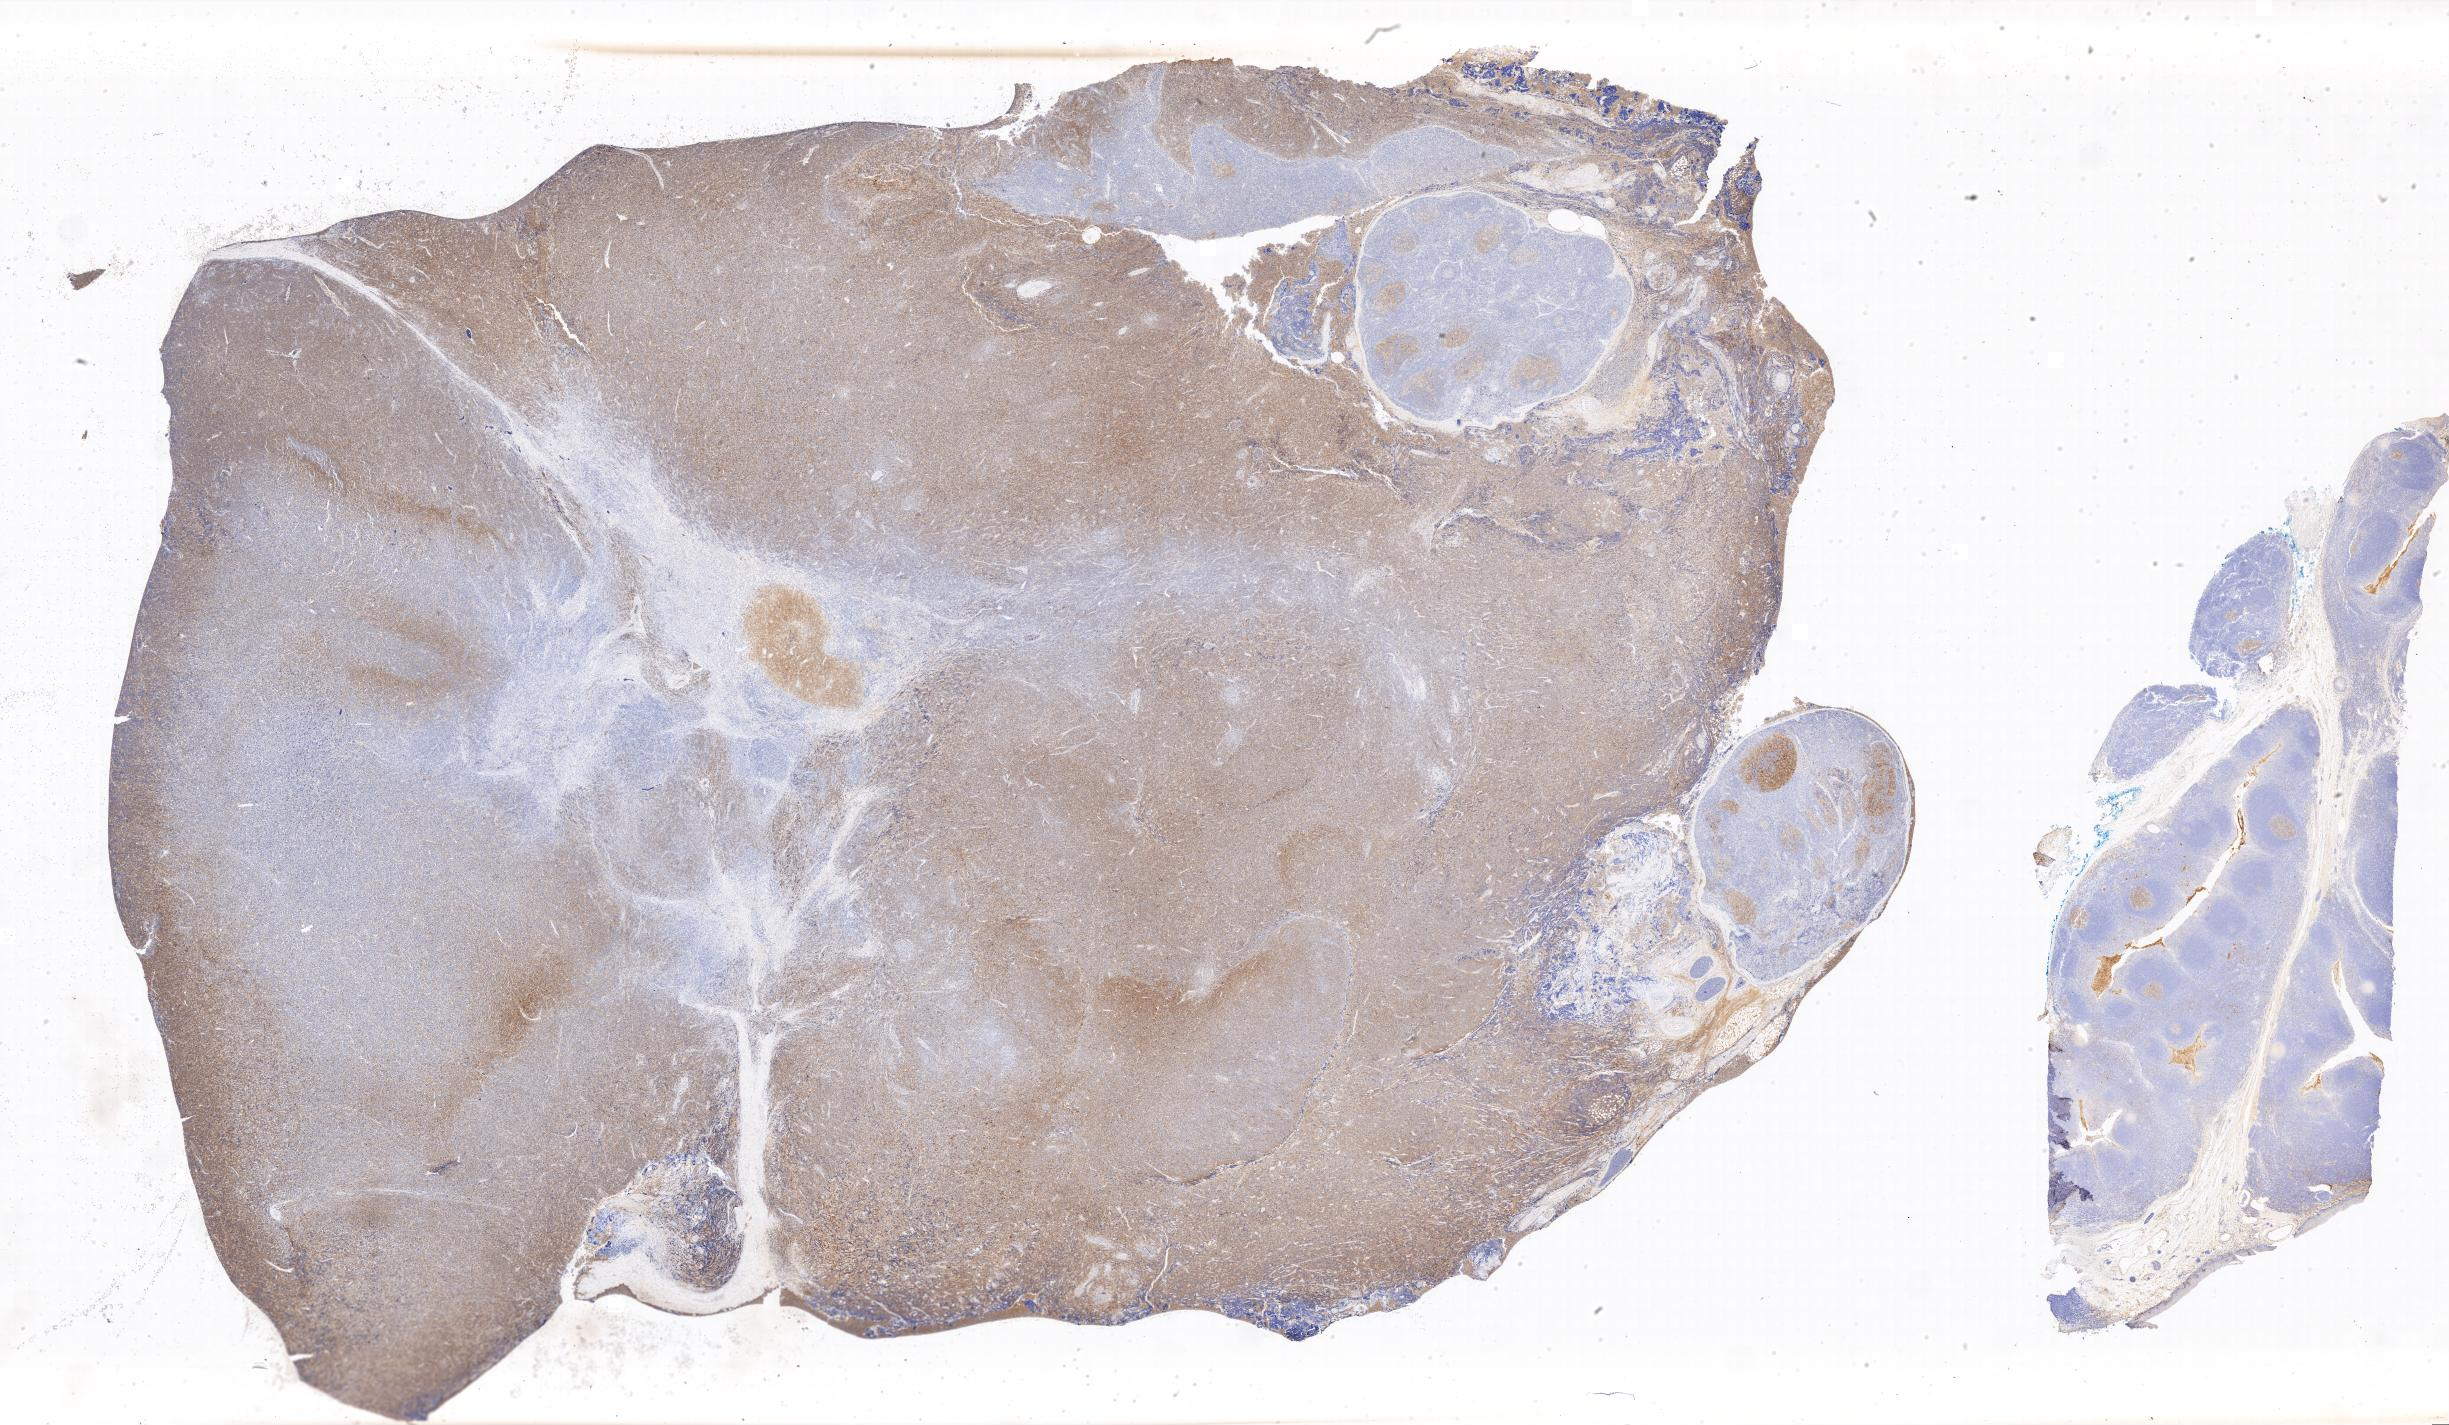
Immunohistochemistry (IHC) whole-slide image stained for CD10 — whole scanned area shown as a low-resolution overview; specimen: tumor tissue; site: lymph node of head and neck. Male, age 3 years at initial diagnosis.
Diagnosis: Burkitt lymphoma, NOS.